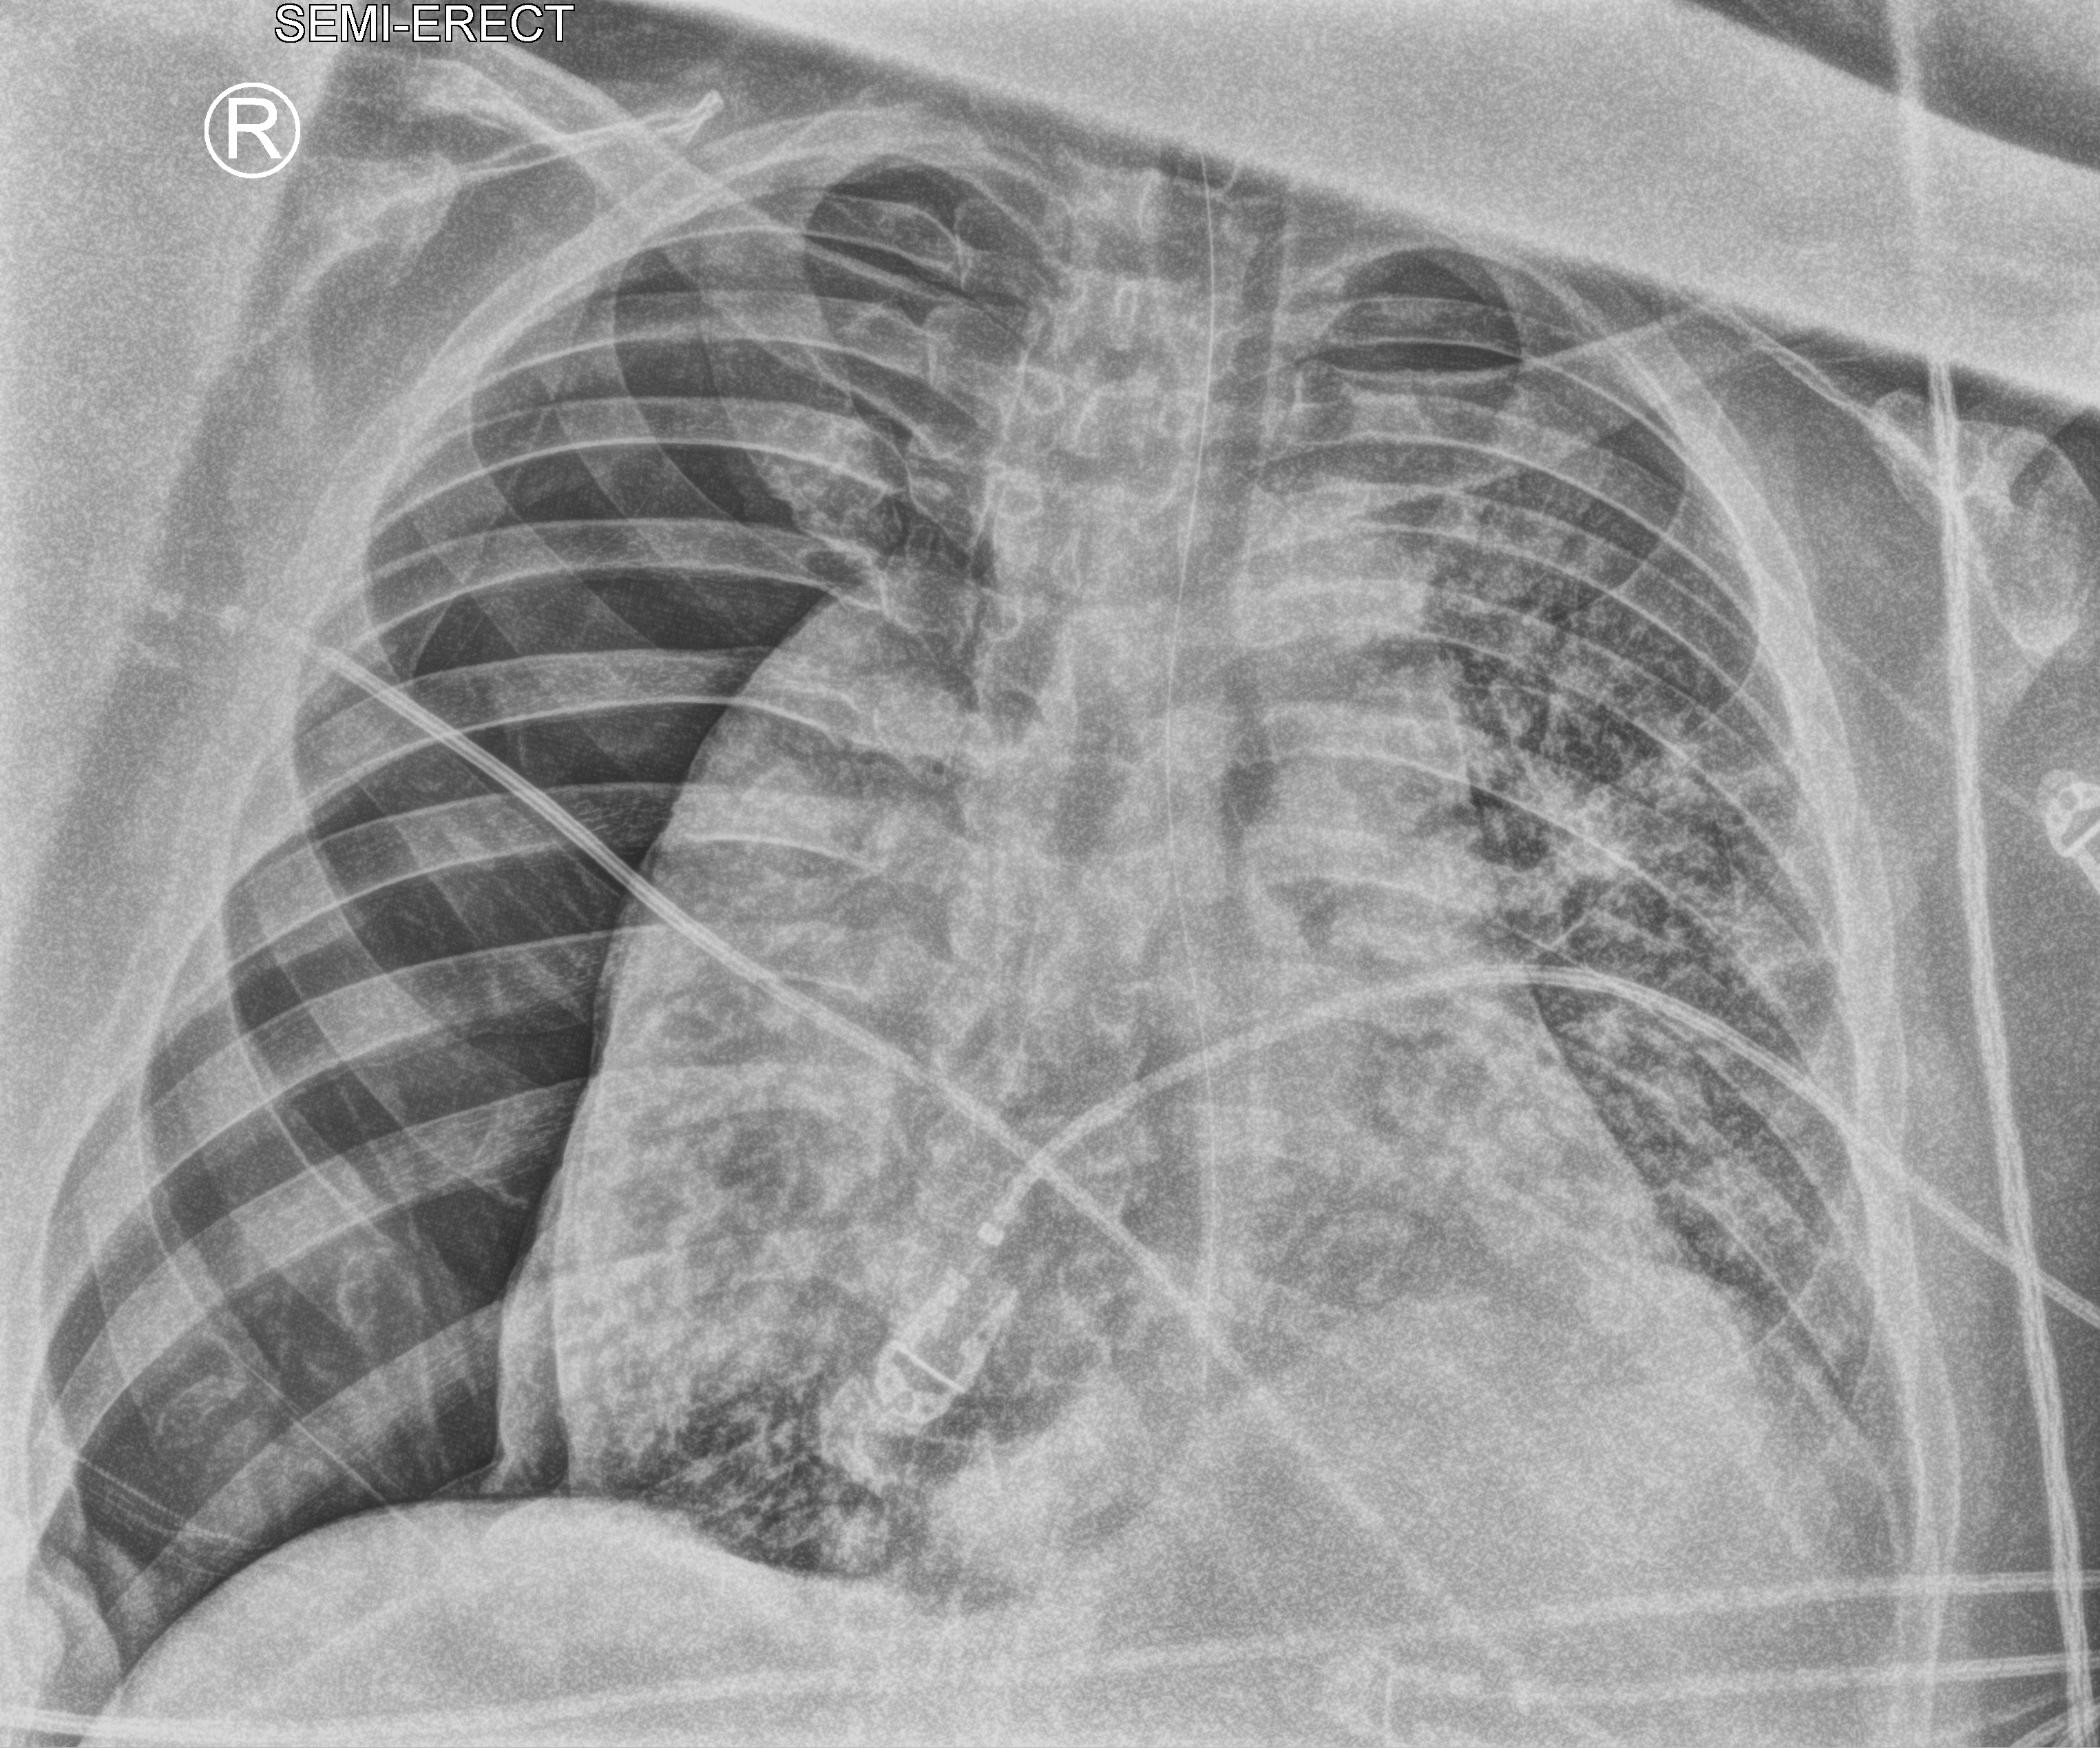
Portable chest radiograph, anteroposterior (AP) projection. Patient hospitalised with COVID-19, aged 18–59 years.
Hospital-stay facts (about this admission, not read from this image; timing relative to this image not recorded):
- admitted to intensive care during this hospital stay: yes
- mechanically ventilated during this hospital stay: yes